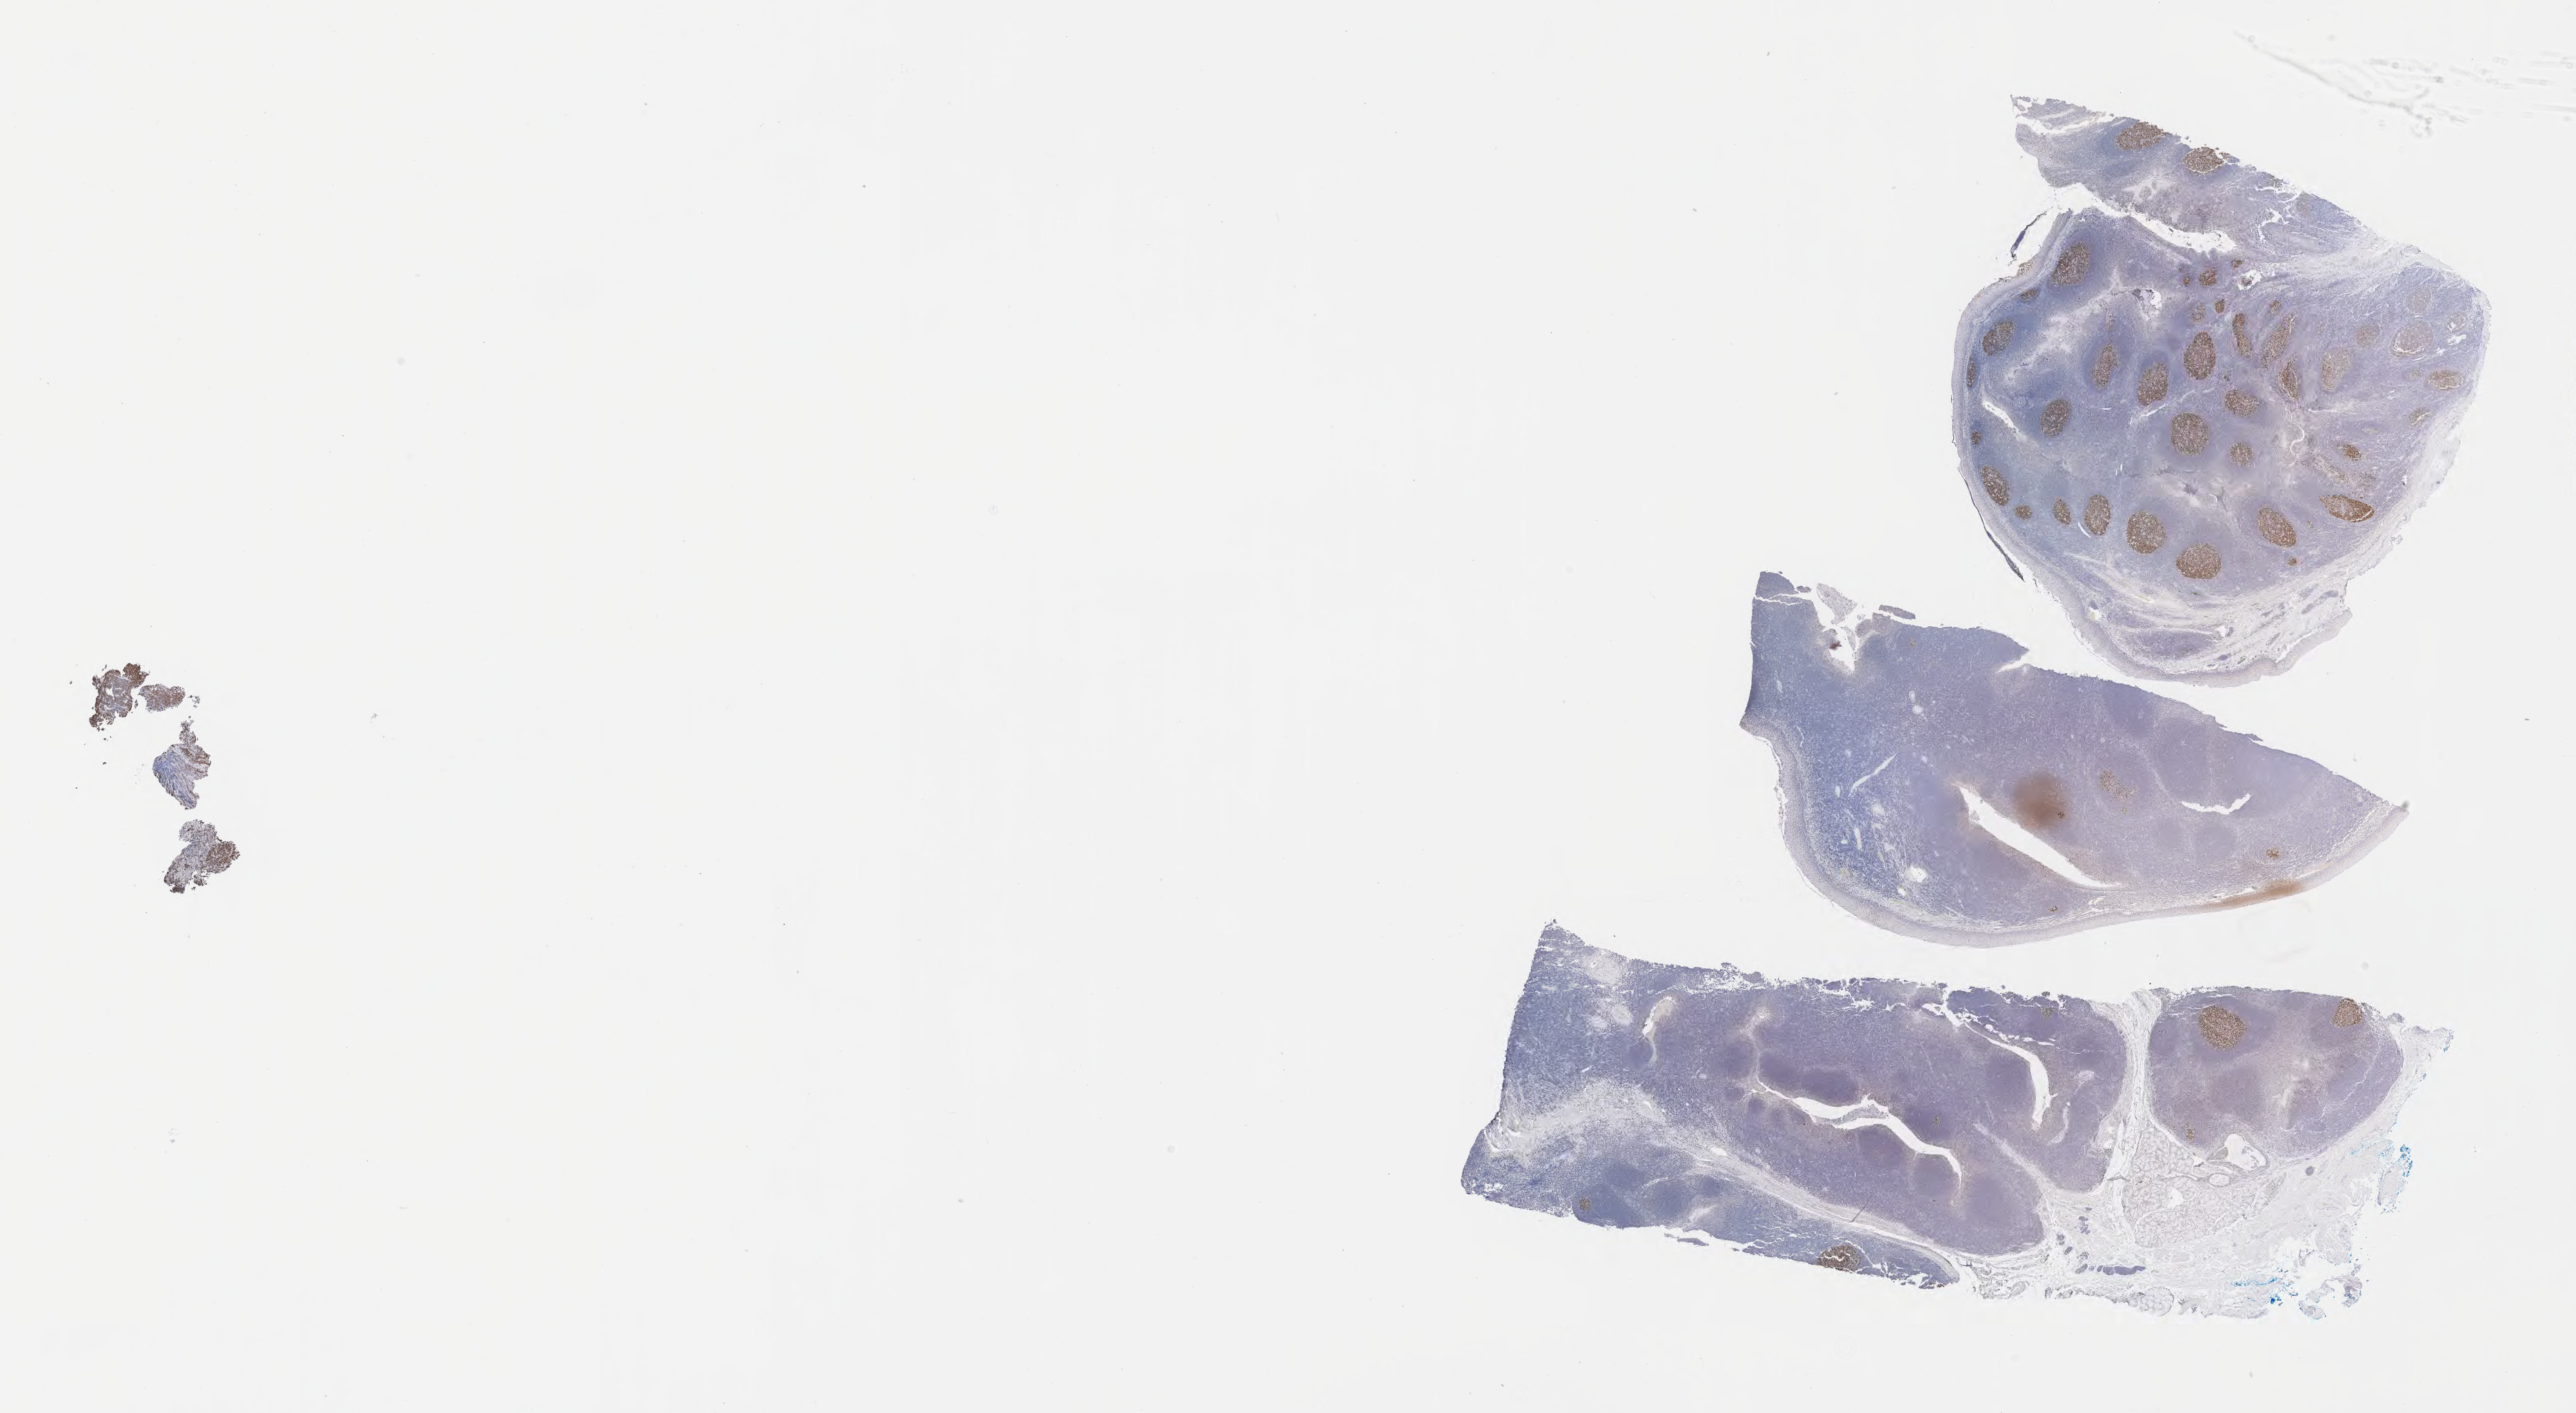
Whole-slide image, immunohistochemical stain for BCL6 — whole scanned area (about 30.2 x 16.6 mm) shown as a low-resolution overview. Tumor tissue. Anatomic site: abdomen proper. Male patient; age at initial diagnosis 6 years.
Histologic diagnosis: Burkitt lymphoma, NOS.